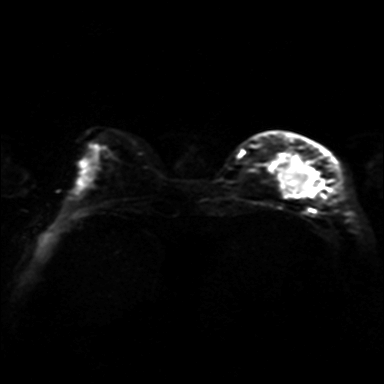
Breast MRI, one axial slice. Slice 11 of 36 in the series (ordered by position). Diffusion-weighted series; image 2 of 4 stored at this slice position (different b-values; order by instance number). 3 T. 384 × 384 image matrix, field of view 320 × 320 mm. Female patient.
Outlined on this slice (manually delineated by an expert):
- tumour on diffusion-weighted imaging: box from (x=283, y=164) to (x=308, y=194) px